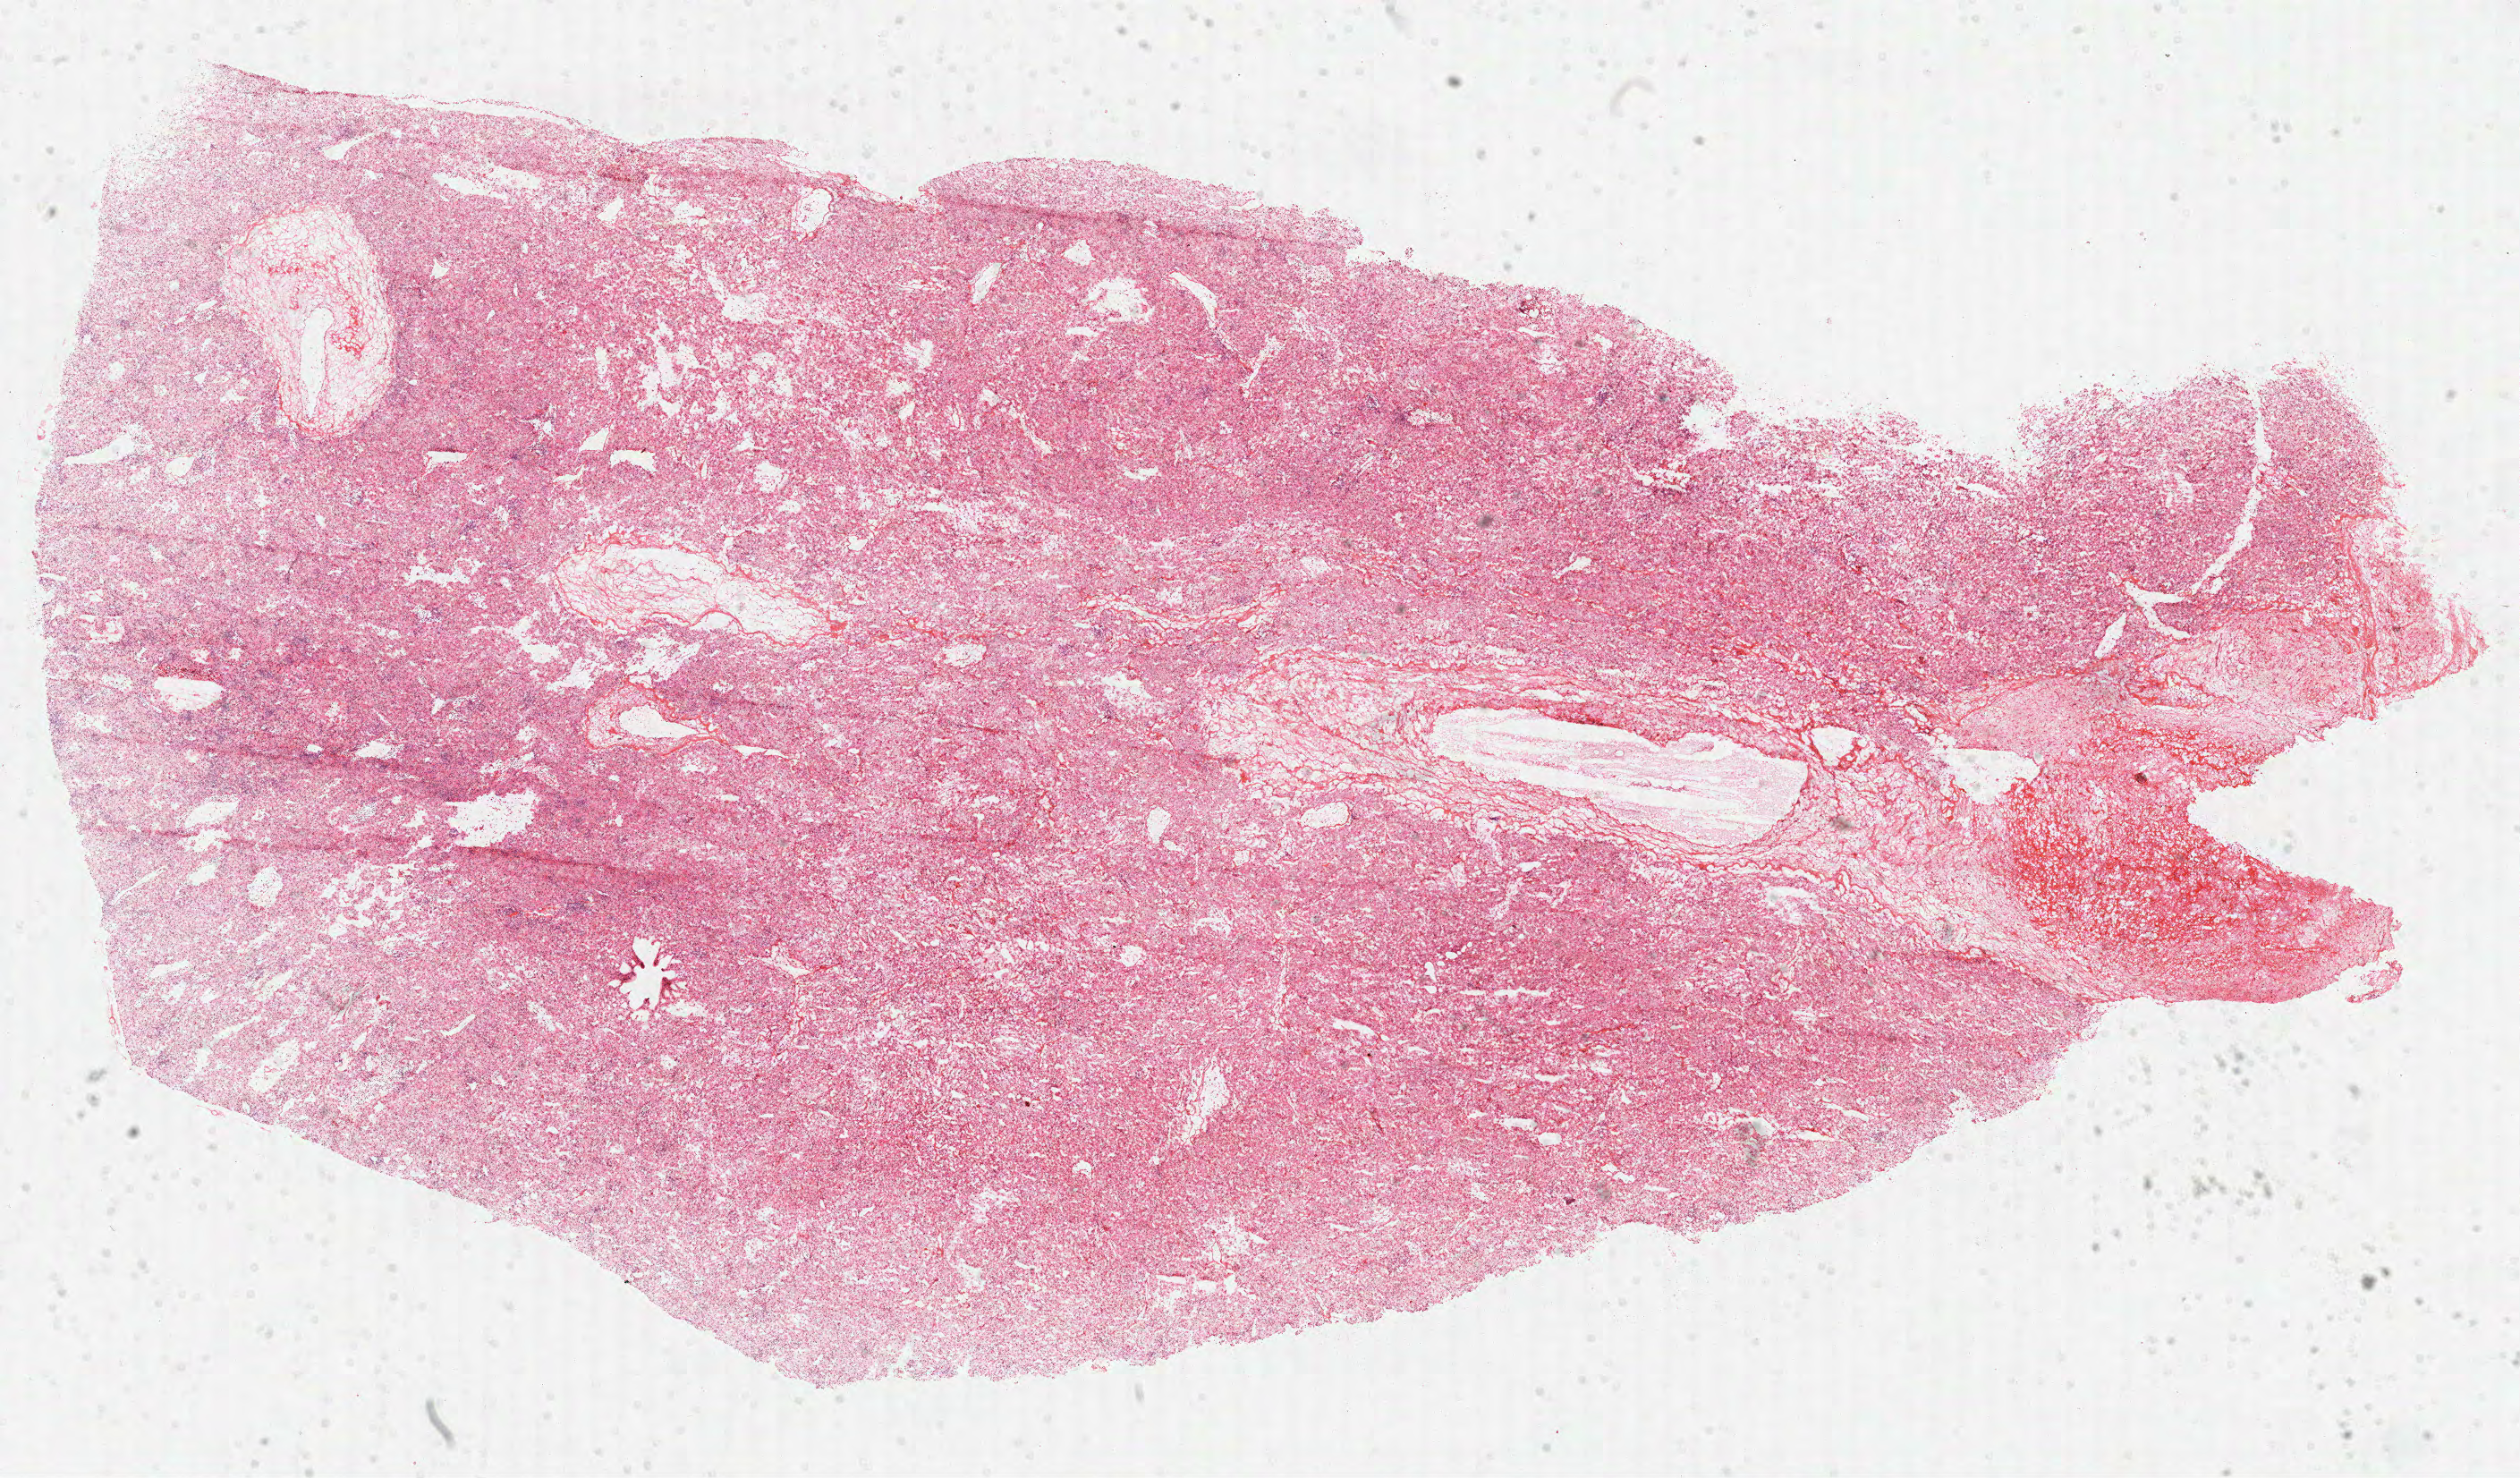
Whole-slide histology image, H&E-stained — low-resolution overview of the scanned area, about 22.7 x 13.3 mm (acquisition: 40x scan), formalin-fixed paraffin-embedded (FFPE) diagnostic section, kidney, primary tumour sample. Male patient; age at initial diagnosis 69 years. Histologic grade: G2 (moderately differentiated).
- AJCC pathologic stage: II (6th edition)
- histologic diagnosis: Clear cell adenocarcinoma, NOS
- lymph nodes positive (case pathology): 0 of 5 examined
- laterality: right